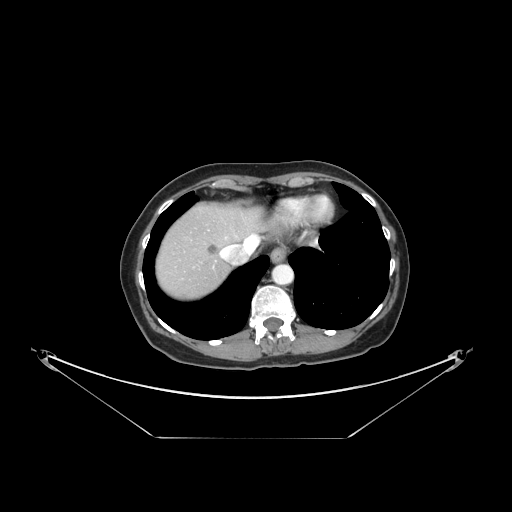
Contrast-enhanced abdominal CT, one axial slice; position 130 of 148 along the scan axis; reconstruction kernel STANDARD; 120 kVp; intravenous contrast given; soft-tissue window (W 400 / L 40 HU); 2.5 mm slice thickness; 512 × 512 image matrix. Female patient, age 73 years. Case-level facts recorded for this patient, not image findings: diagnosis: colorectal cancer liver metastases, imaged before liver resection; multiple liver metastases: no; largest metastasis: 1 cm; disease in both lobes: no.
Structures marked on this image (manually delineated by an expert):
- liver: box from (x=156, y=204) to (x=261, y=300) px
- planned liver remnant (the part of the liver to remain after resection): (x=185, y=204)–(x=259, y=244)
- liver metastasis: (x=207, y=244)–(x=218, y=256)